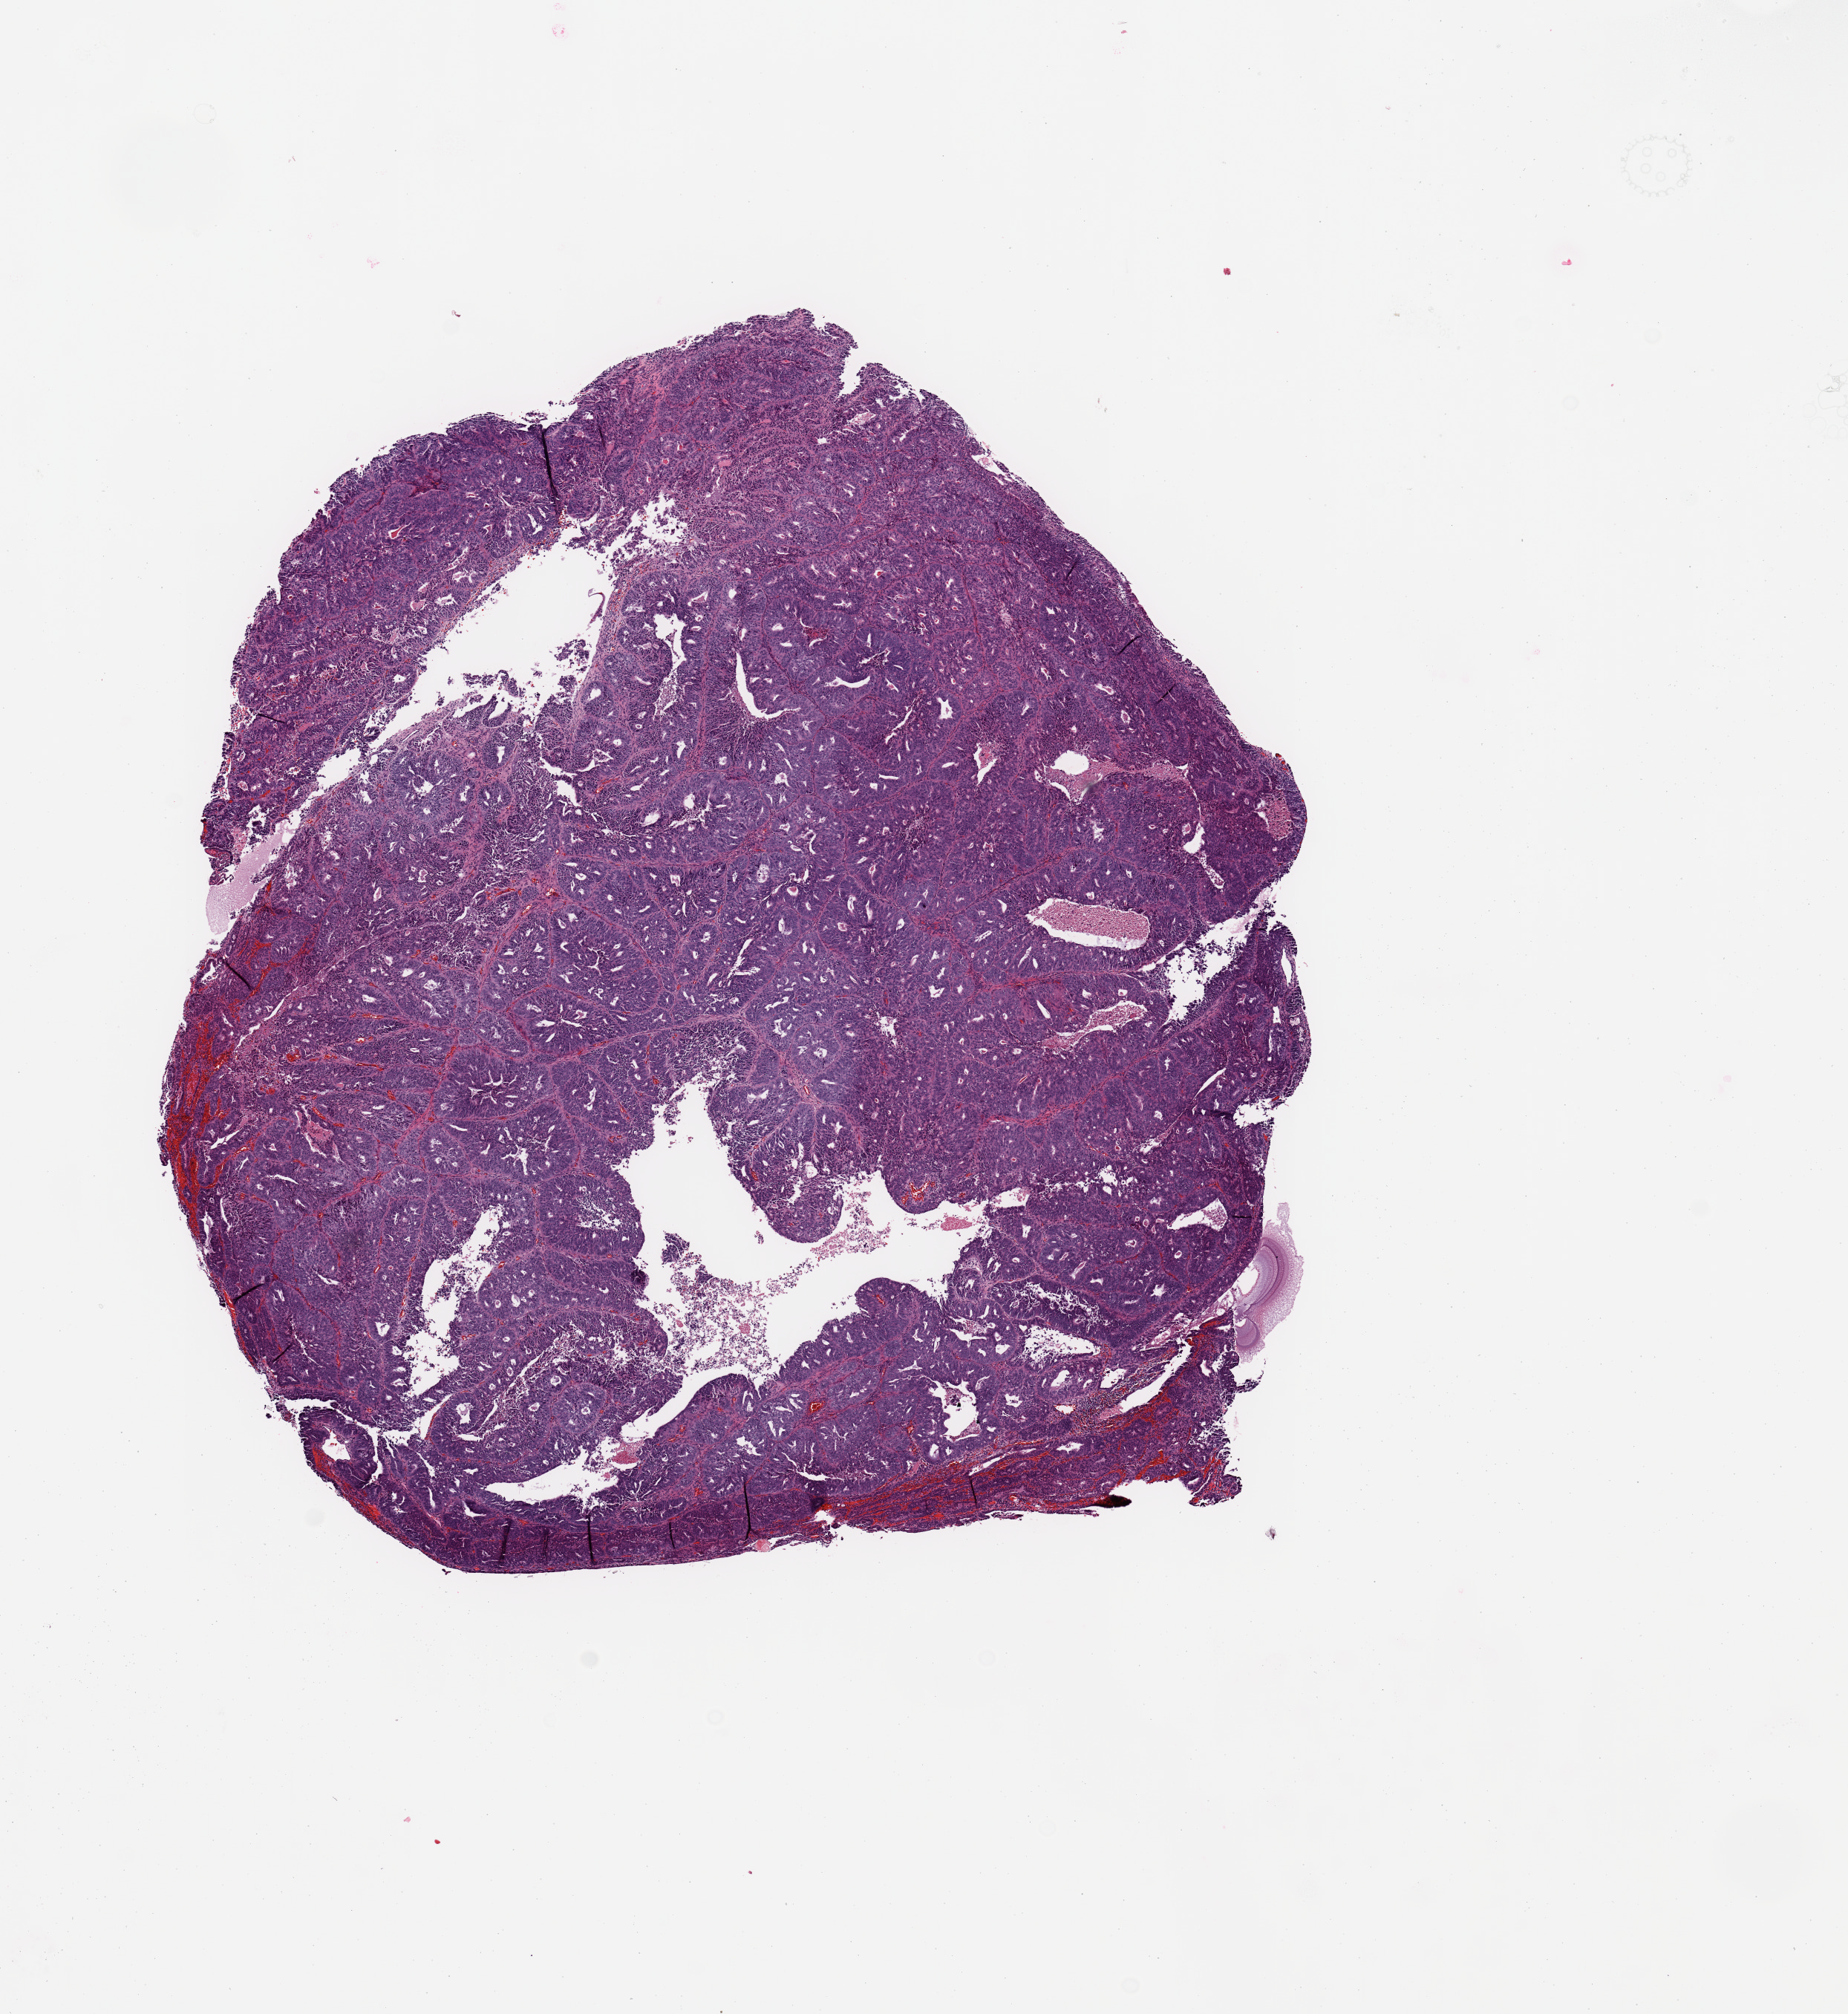
Whole-slide histology image, H&E-stained — low-resolution overview of the scanned area, about 9.8 x 10.7 mm (acquisition: 20x scan); tumour tissue sample, sampled site: uterus. Patient: female, age 75 years. Histologic grade: G2 (moderately differentiated). Pathologist review of this section (percent, as recorded): tumour nuclei 95%, necrosis 5%.
Histologic diagnosis: Endometrioid adenocarcinoma, NOS. AJCC pathologic stage: I.